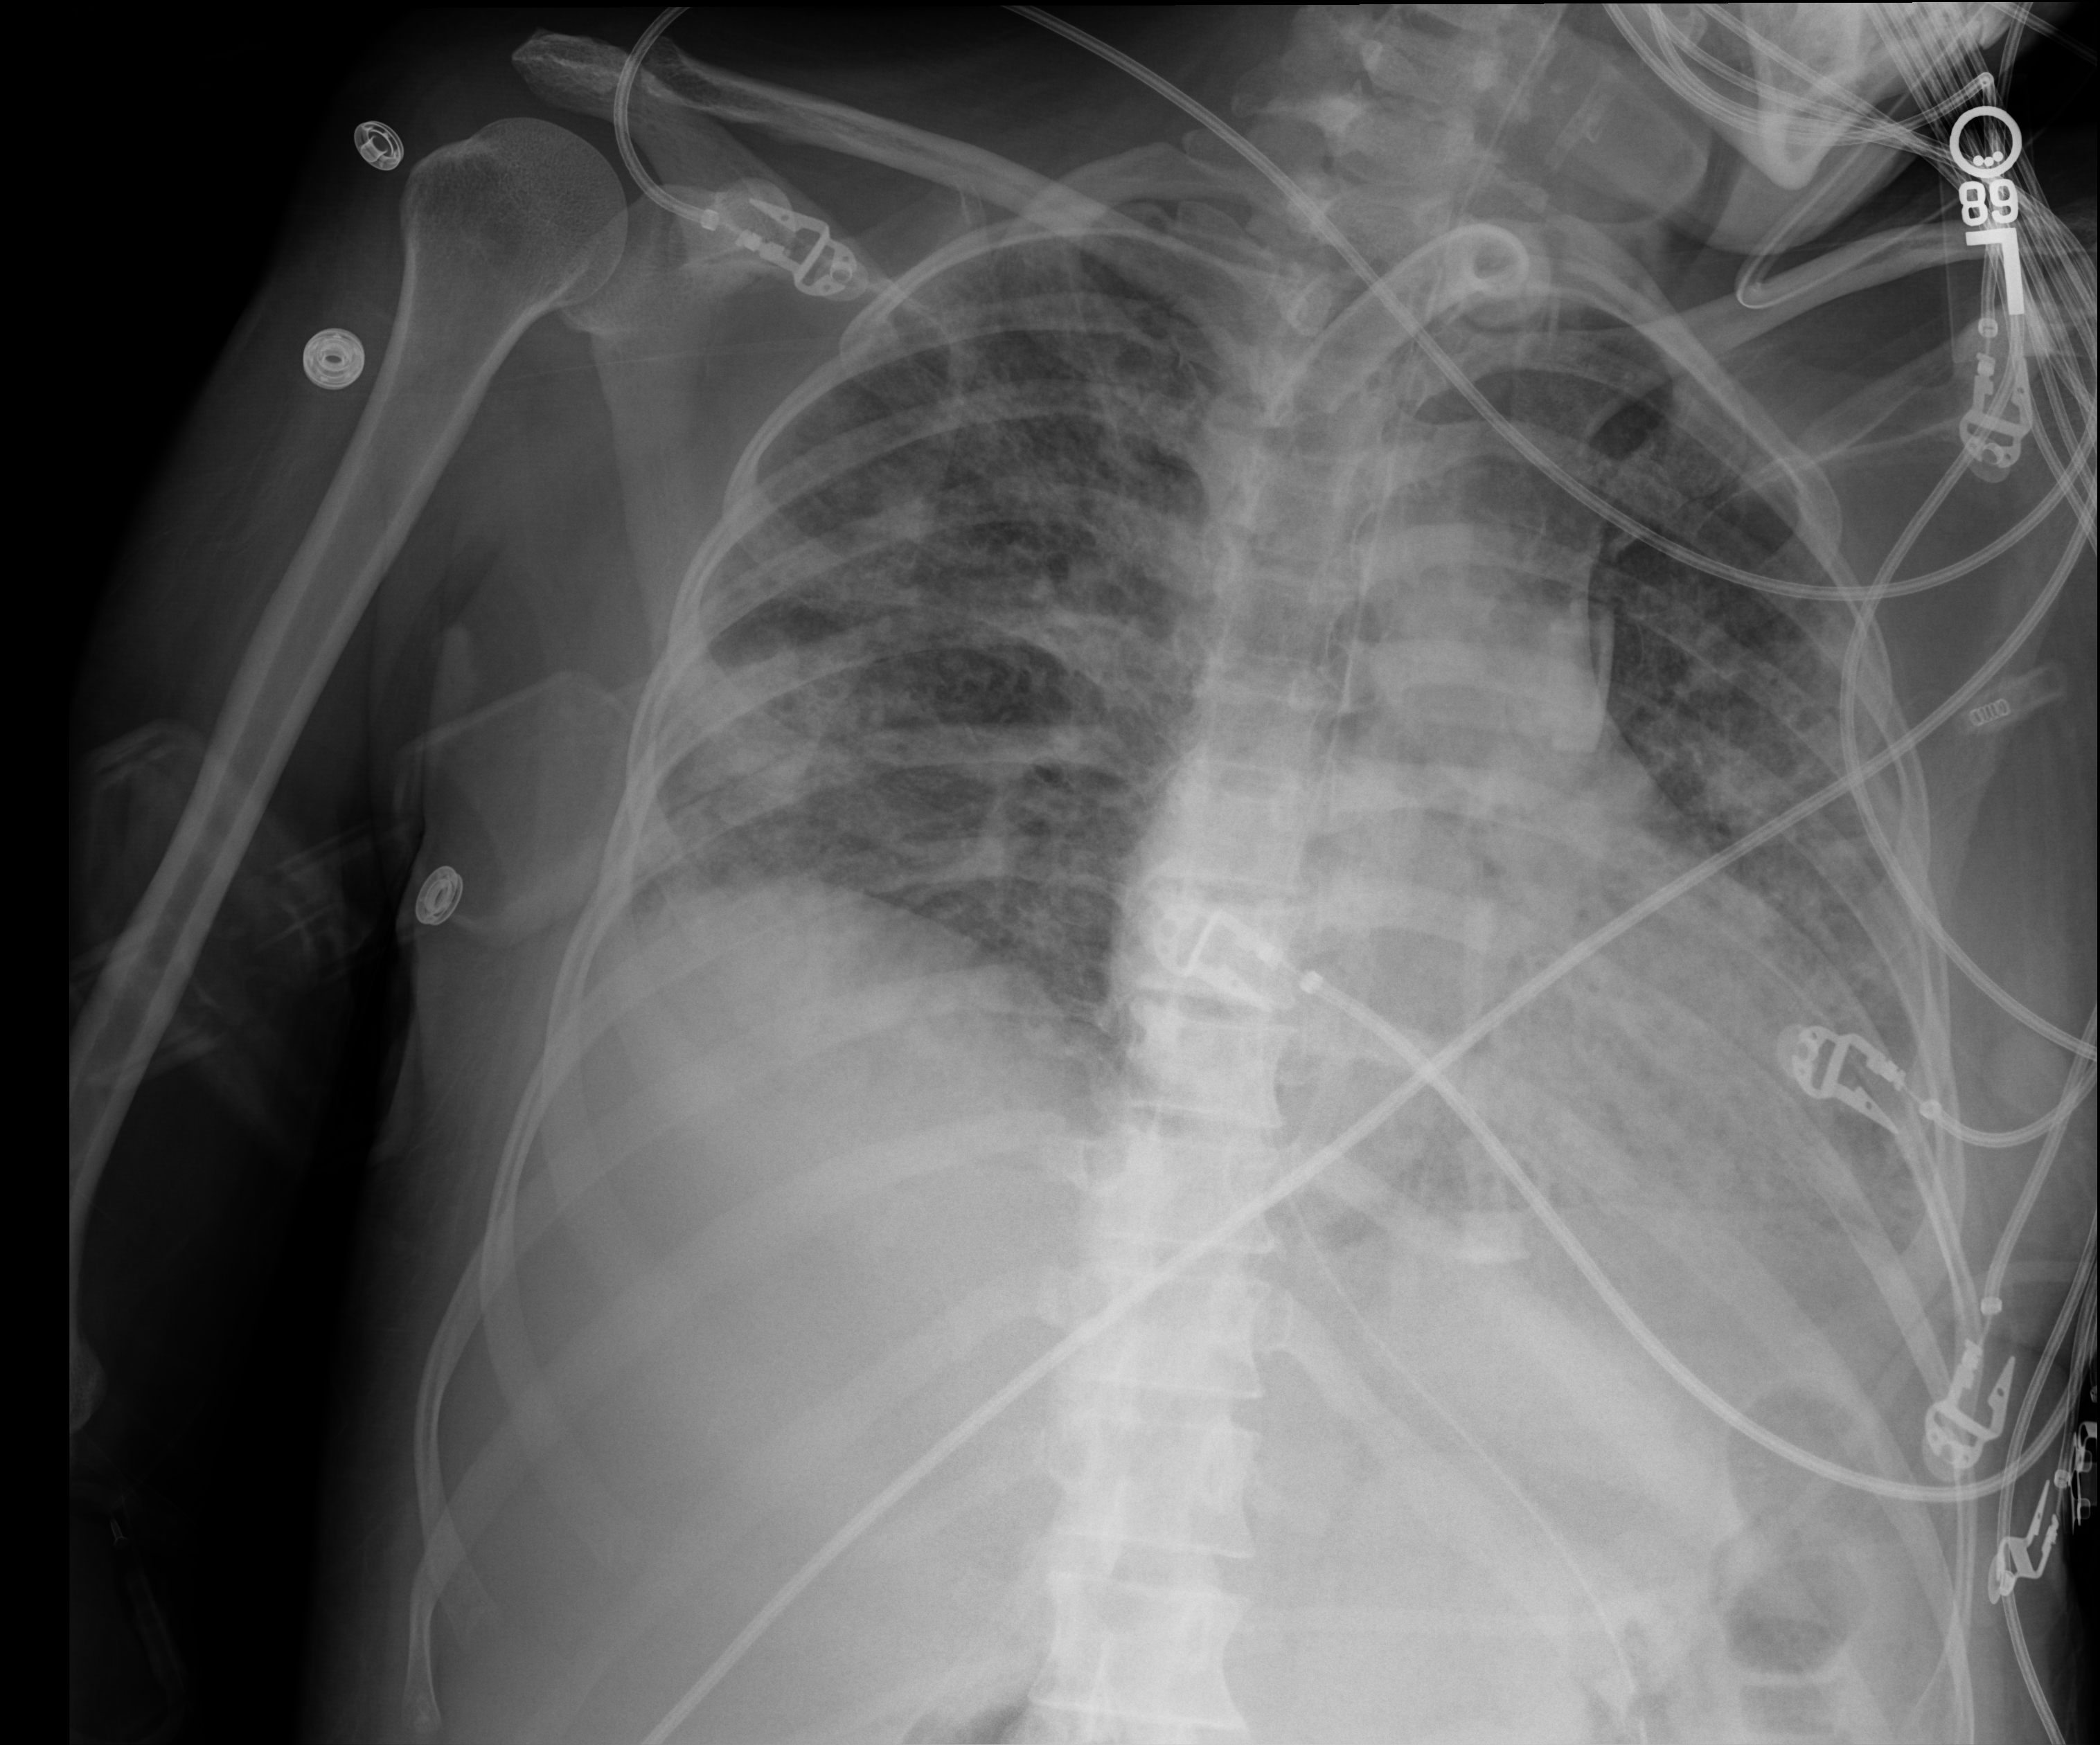
Portable chest radiograph; anteroposterior (AP) projection. Patient hospitalised with COVID-19; female, aged 18–59 years.
Admission-level facts for this patient (not findings on this image; timing relative to this image not recorded): length of hospital stay: 71 days.